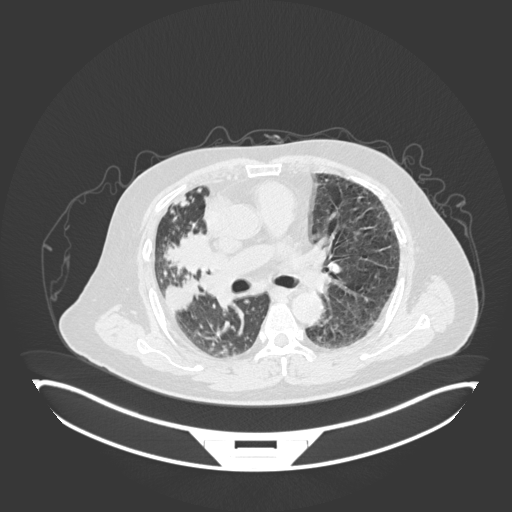
Chest CT, one axial slice; slice 94 of 201 in the series (ordered by position); reconstruction kernel B30f; lung window (W 1500 / L -600 HU); 512 × 512 image matrix, field of view 500 × 500 mm. Patient: male, 69 years. From the clinical record (not read from this slice): clinical TNM (as recorded): T4 N3 M1.
Structures marked on this image (rectangle marked by the reading radiologist):
- lung tumour (recorded histology: adenocarcinoma): bounding box <165,229,212,278> (left, top, right, bottom; pixels)